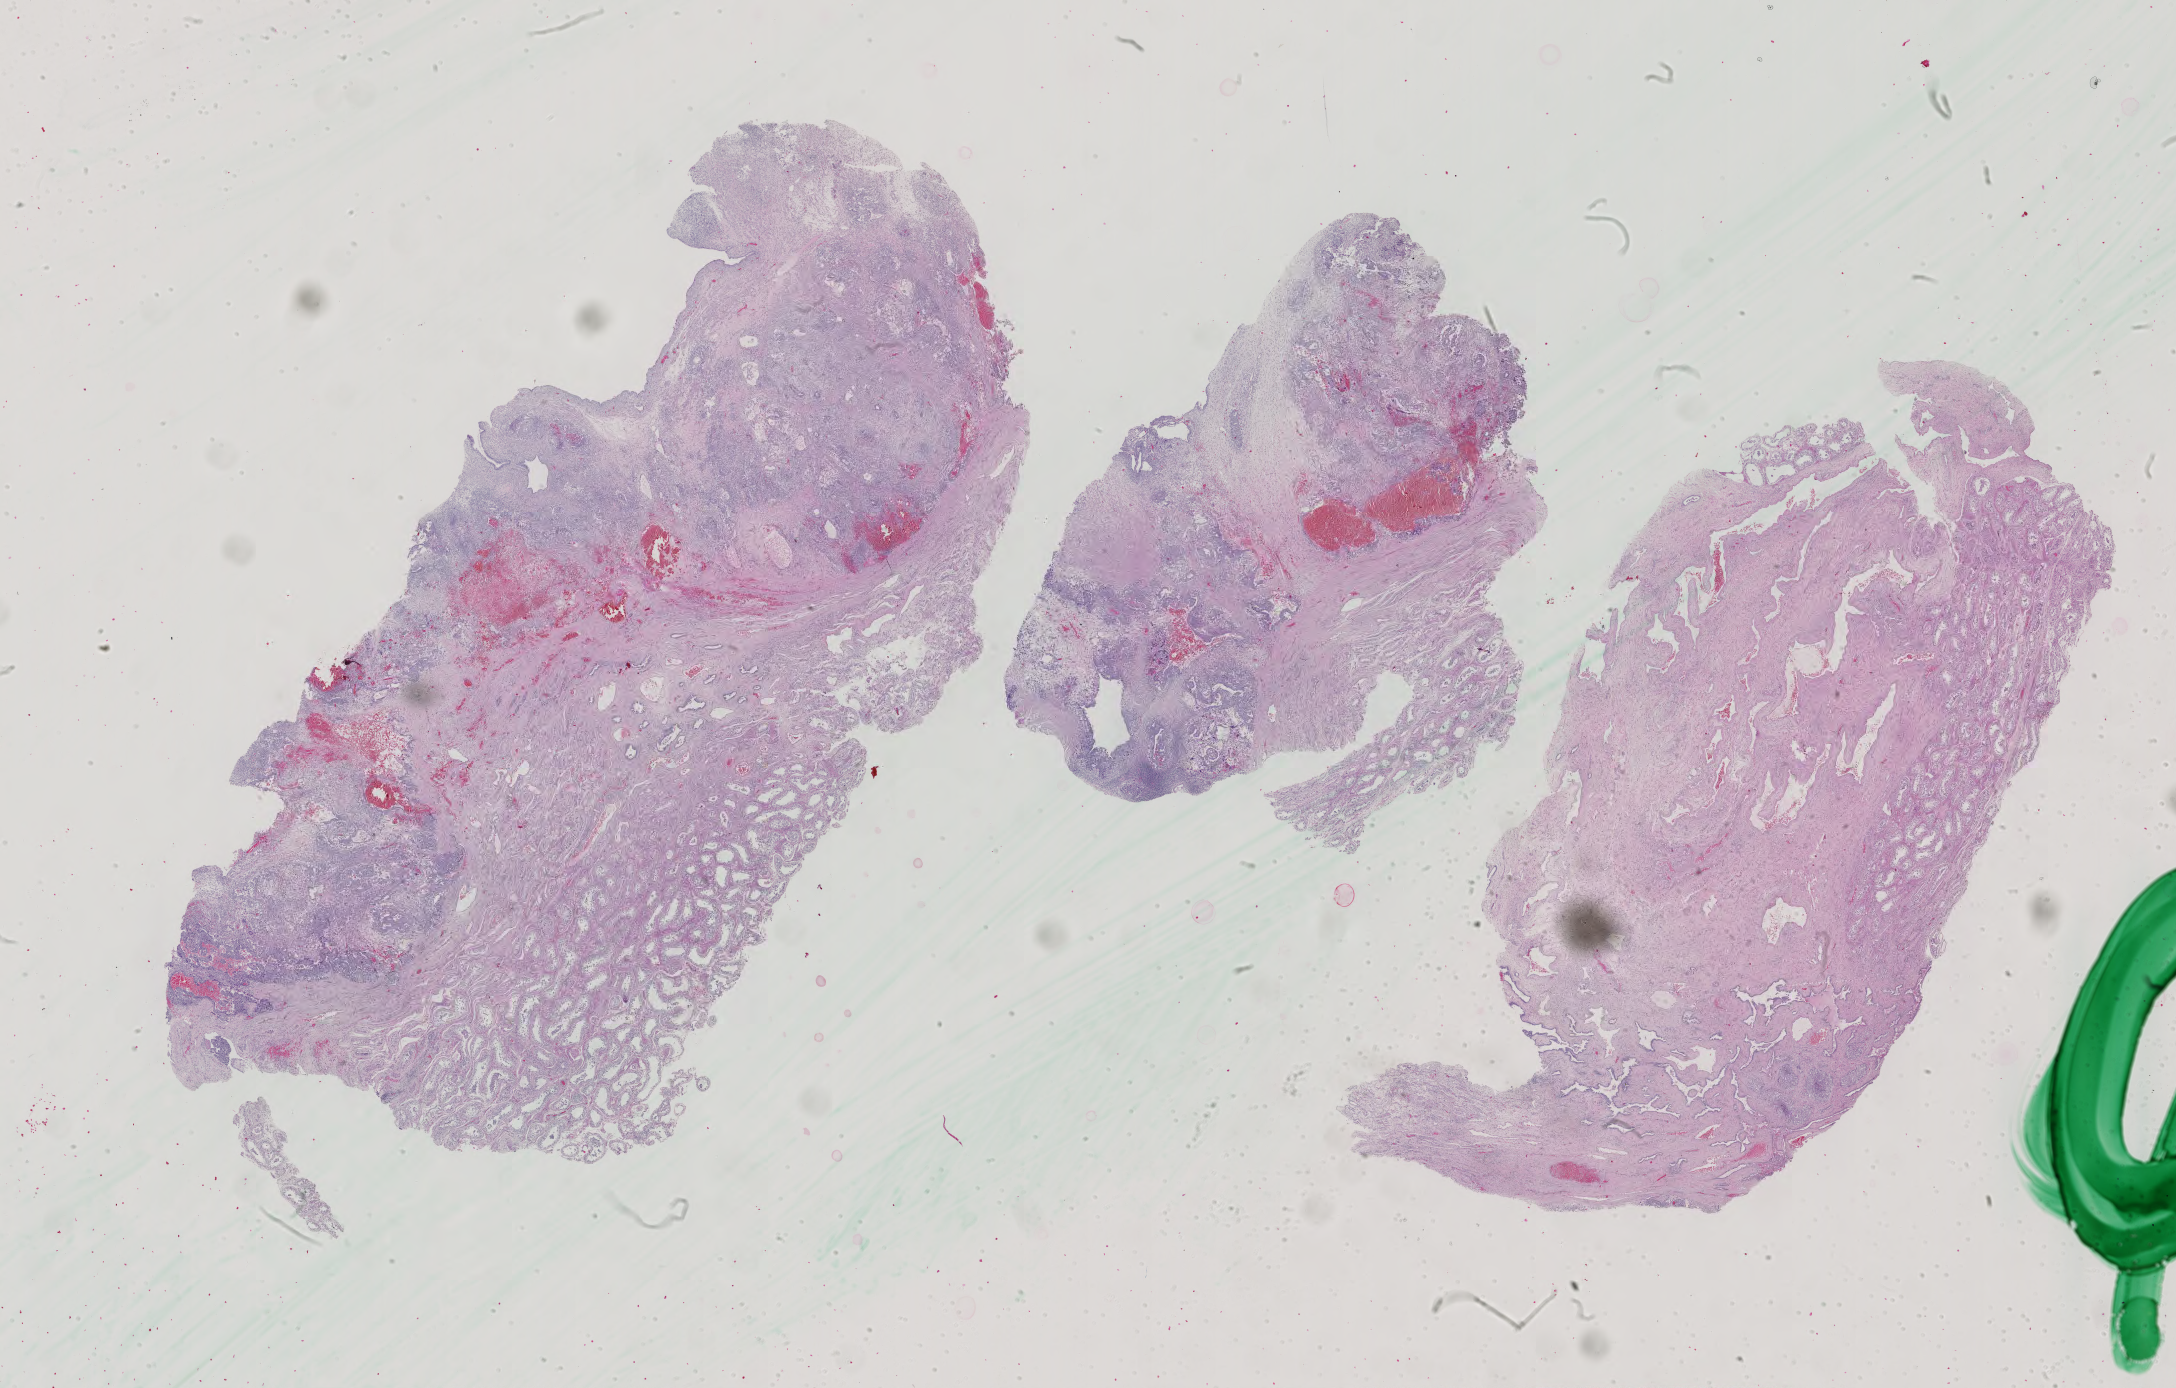
H&E-stained whole-slide image — shown as a low-resolution overview of the whole scanned area (about 31.7 x 20.2 mm). FFPE section. Testis, primary tumour sample. Male patient; age at initial diagnosis 28 years.
Diagnosis: Mixed germ cell tumor.